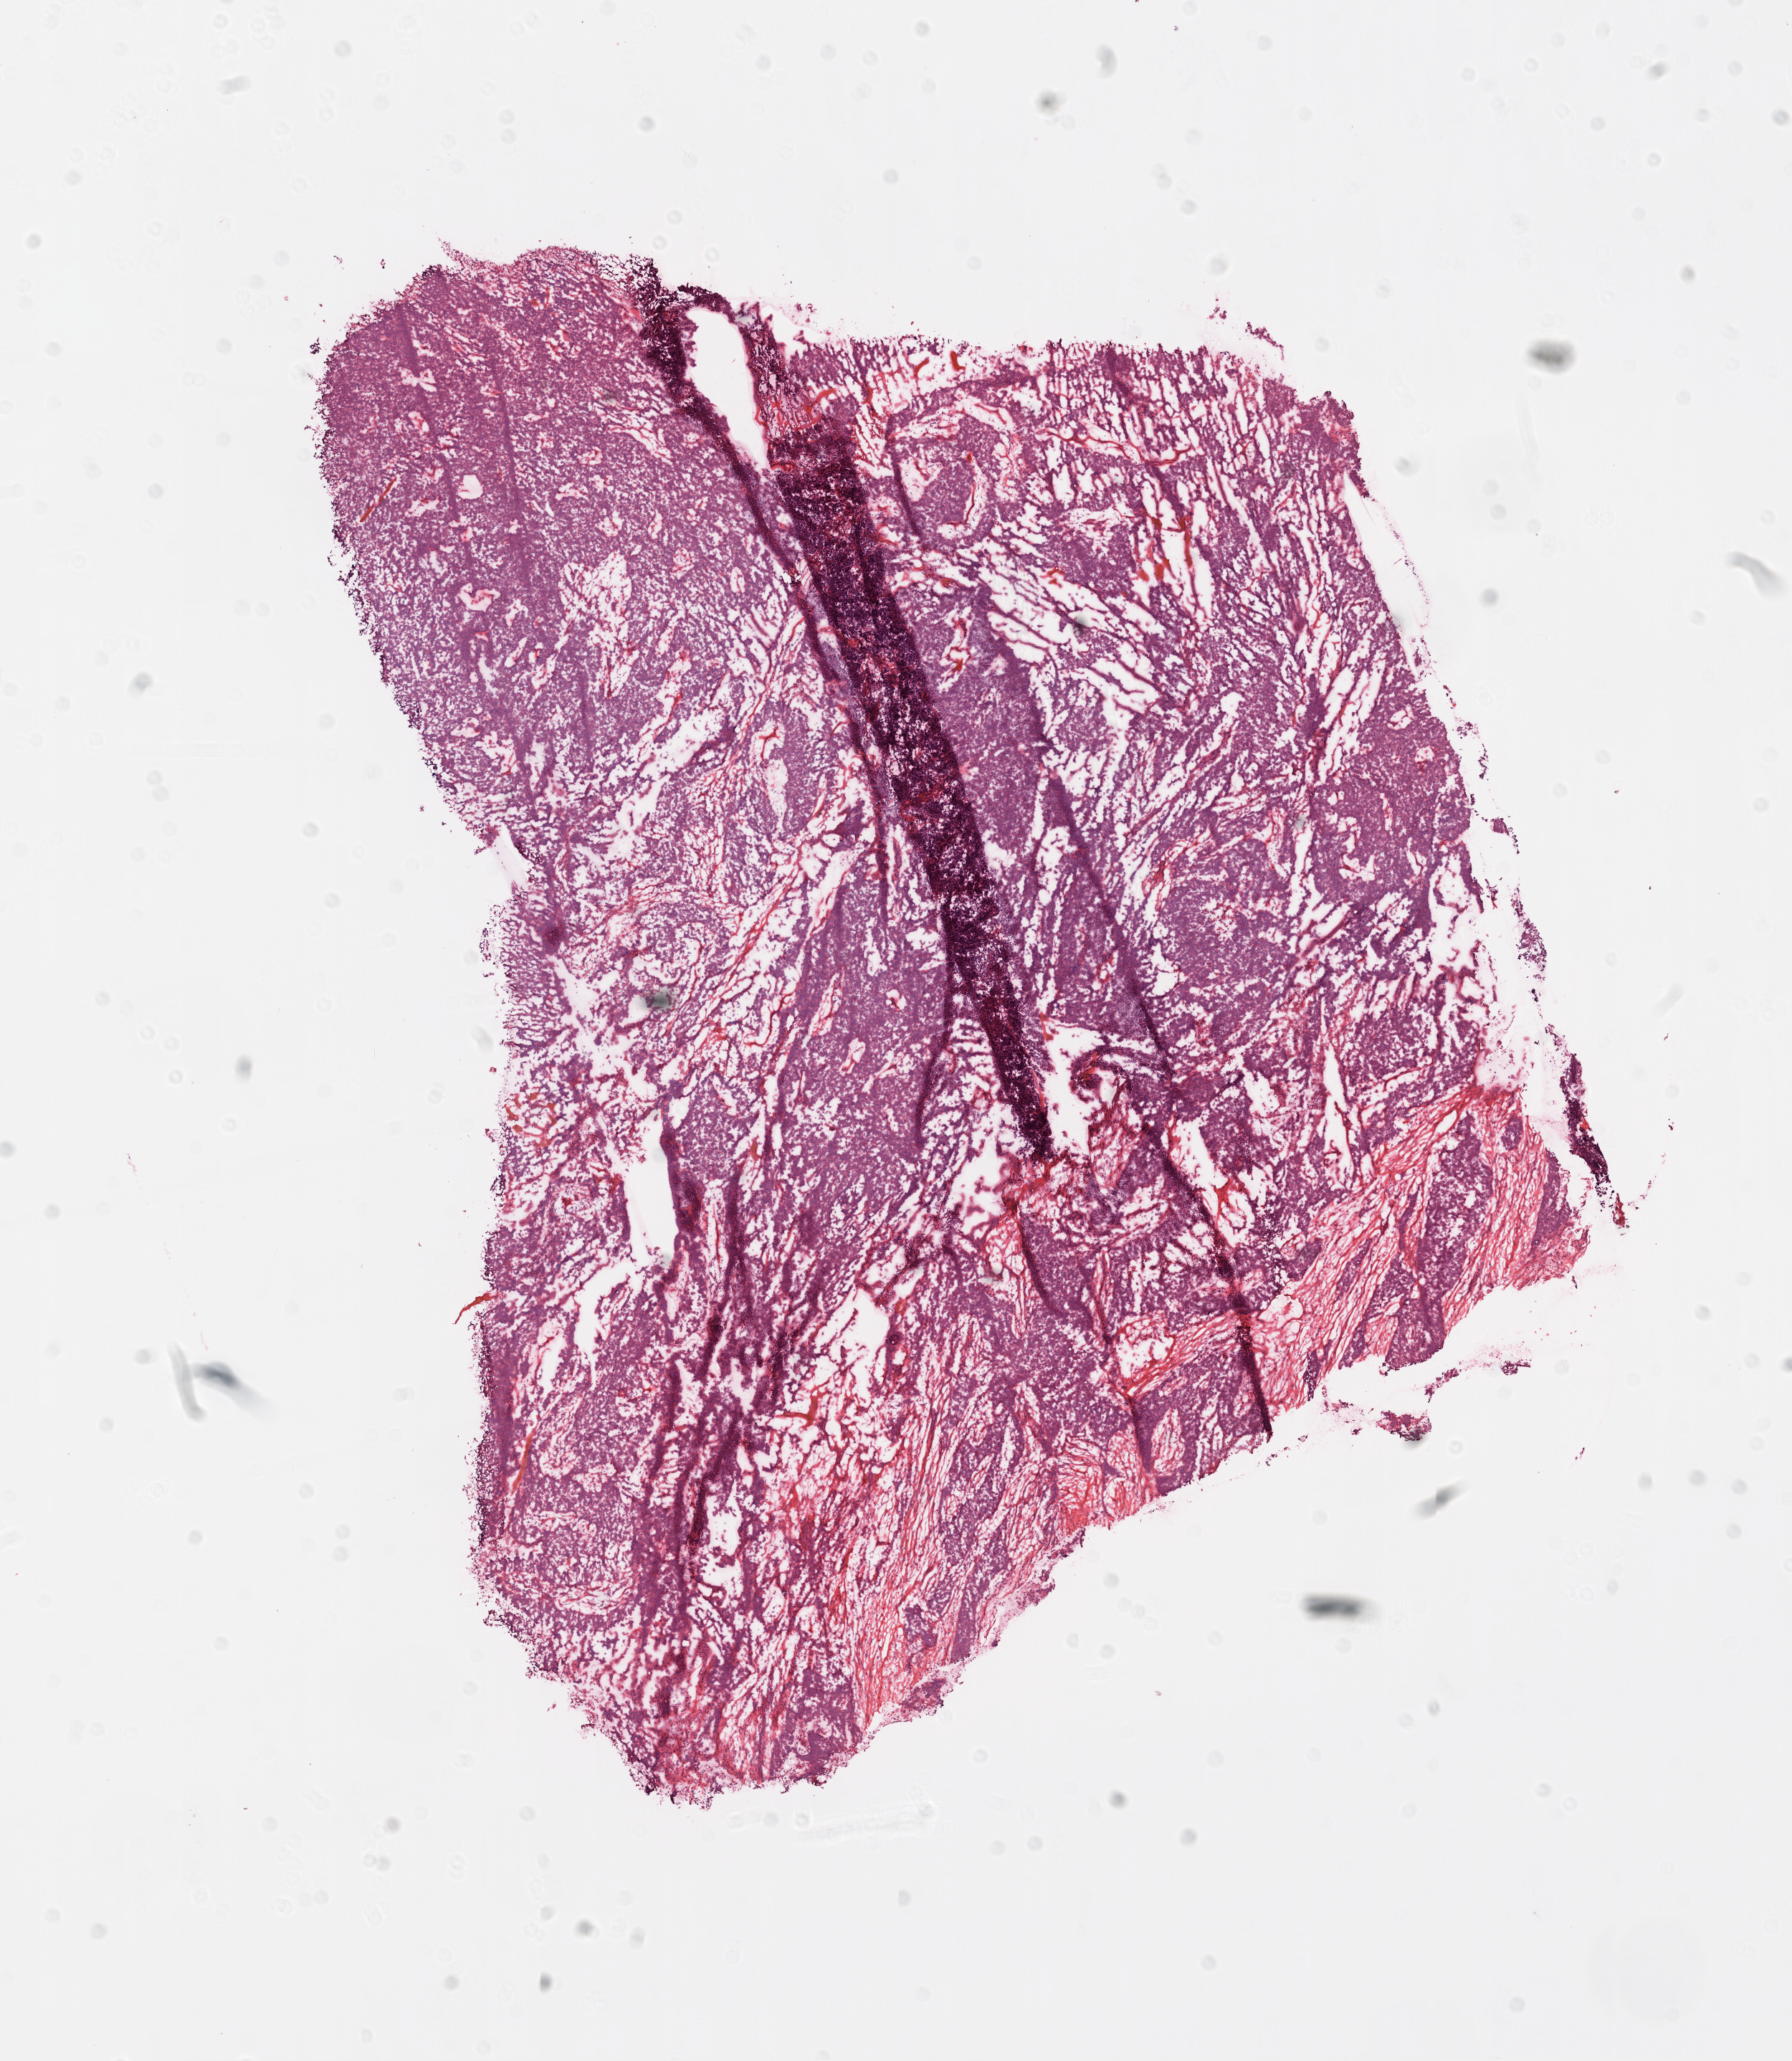
Whole-slide histology image, H&E-stained, a low-resolution overview of the entire scanned area, about 10.0 x 11.5 mm; frozen section from the top of the tissue portion; sample: primary tumour, ovary. Patient: female, age at initial diagnosis 48 years. Slide review estimates, as recorded: tumour cells 95%, tumour nuclei 95%.
Diagnosis: Serous cystadenocarcinoma, NOS.